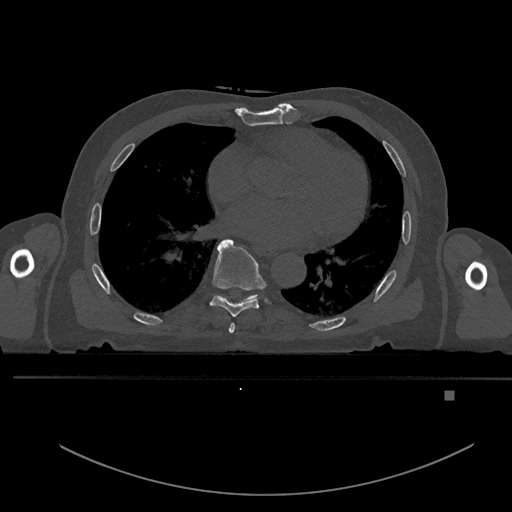
CT including the spine, one axial slice; position 248 of 969 along the scan axis; bone window (W 1800 / L 400 HU); 0.5 mm slice thickness; 512 × 512 image matrix, field of view 456 × 456 mm. Male patient, age 82 years. From the clinical record (not read from this slice): primary cancer: prostate.
Annotated regions visible in this slice (semi-automatically segmented with operator editing):
- T6 vertebra: bounding box [x1, y1, x2, y2] px = [229, 323, 235, 334]
- T7 vertebra: [209, 239, 265, 317]
- T8 vertebra: [215, 294, 258, 304]